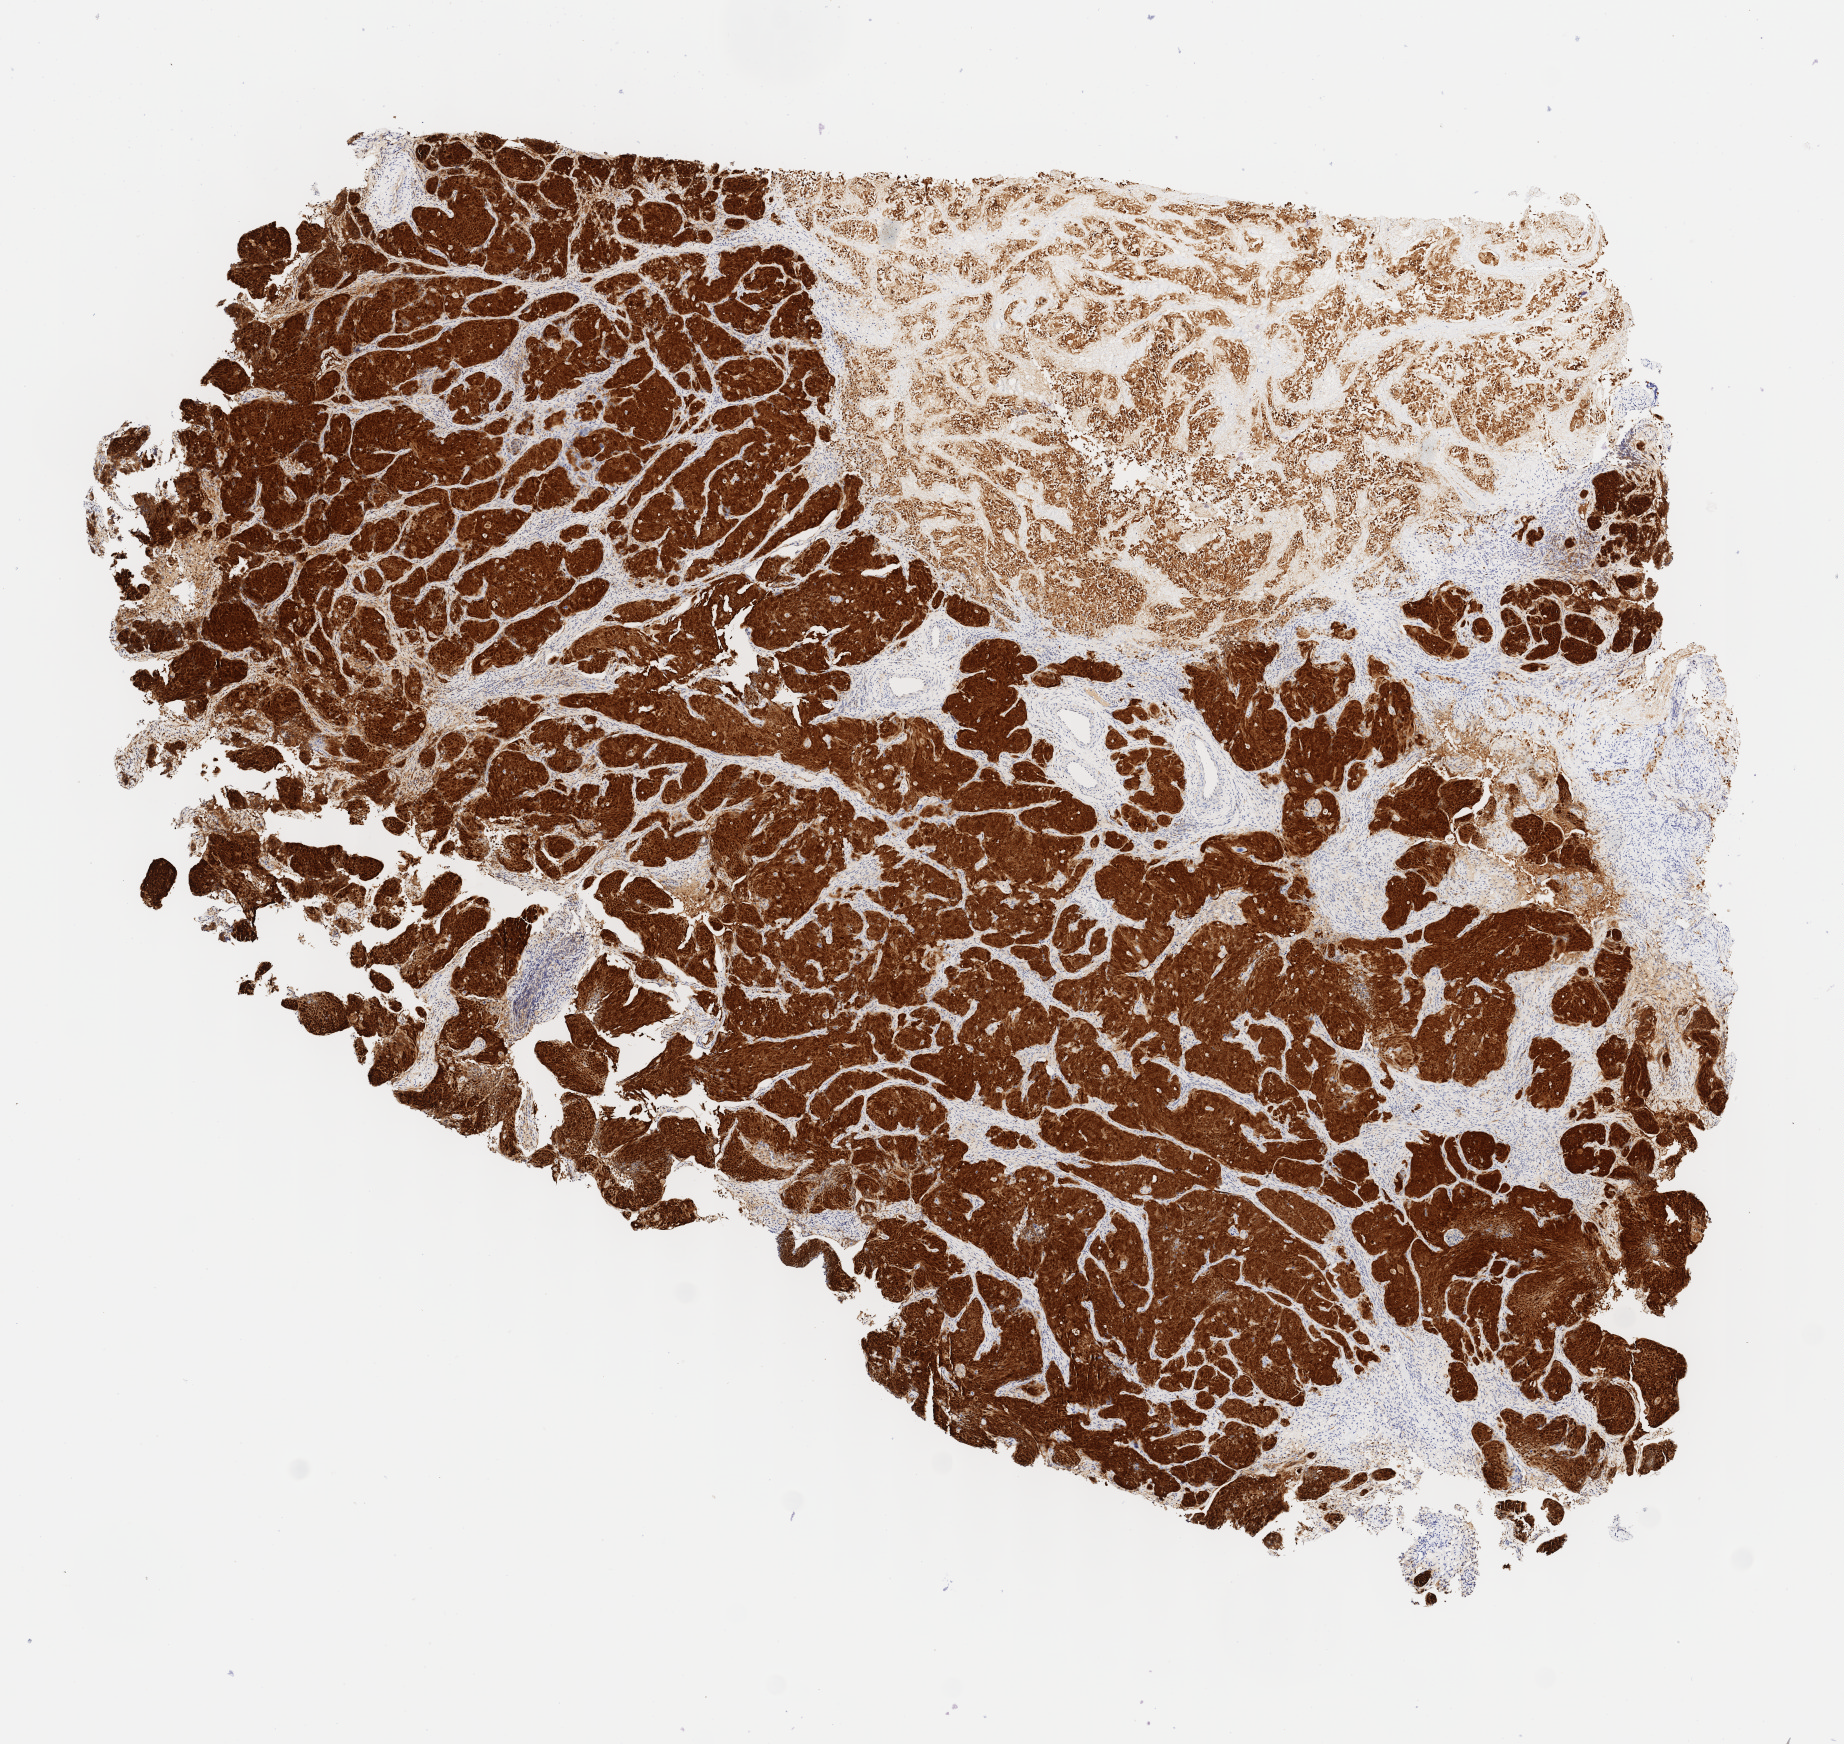
Whole-slide image, immunohistochemical stain for p16 (p16INK4a), a low-resolution overview of the entire scanned area, about 7.3 x 6.9 mm; specimen: tumor tissue; anatomic site: cervix. Patient female; 53 years old.
Diagnosis: Squamous cell carcinoma, large cell, nonkeratinizing, NOS.